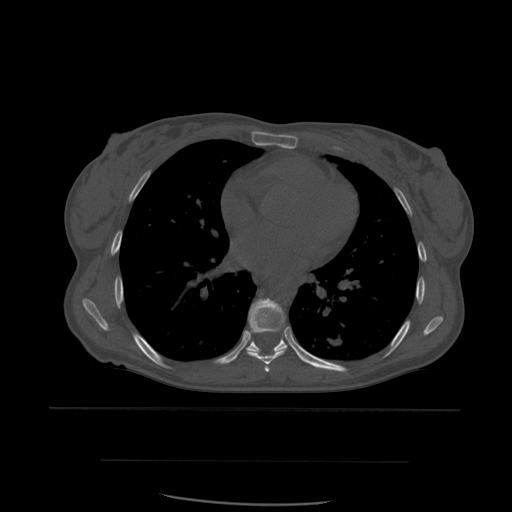
CT including the spine, one axial slice. Slice 367 of 574 in the series (ordered by position). Bone window (W 1800 / L 400 HU). 1.25 mm slice thickness. 512 × 512 image matrix, field of view 392 × 392 mm. Patient age 48 years. From the clinical record (not read from this slice): primary cancer: lung.
Structures marked on this image (semi-automatic segmentation, software-assisted and operator-edited):
- T6 vertebra: bounding box (x1, y1, x2, y2) in pixels: (265, 367, 269, 372)
- T7 vertebra: (247, 299, 288, 372)
- T8 vertebra: (247, 334, 288, 354)